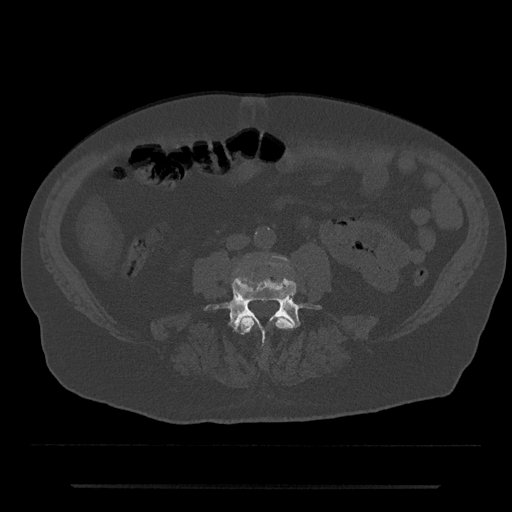
CT including the spine, one axial slice; position 367 of 797 along the scan axis; reconstruction kernel Br40s/3; 120 kVp; bone window (W 1800 / L 400 HU); 512 × 512 image matrix, field of view 434 × 434 mm. Male patient, age 80 years. From the clinical record (not read from this slice): primary cancer: prostate; vertebrae with lytic lesions (as recorded): L1, T11.
Annotated regions visible in this slice (semi-automatic segmentation, software-assisted and operator-edited):
- L3 vertebra: box from (x=237, y=316) to (x=294, y=334) px
- L4 vertebra: (x=205, y=277)–(x=321, y=344)